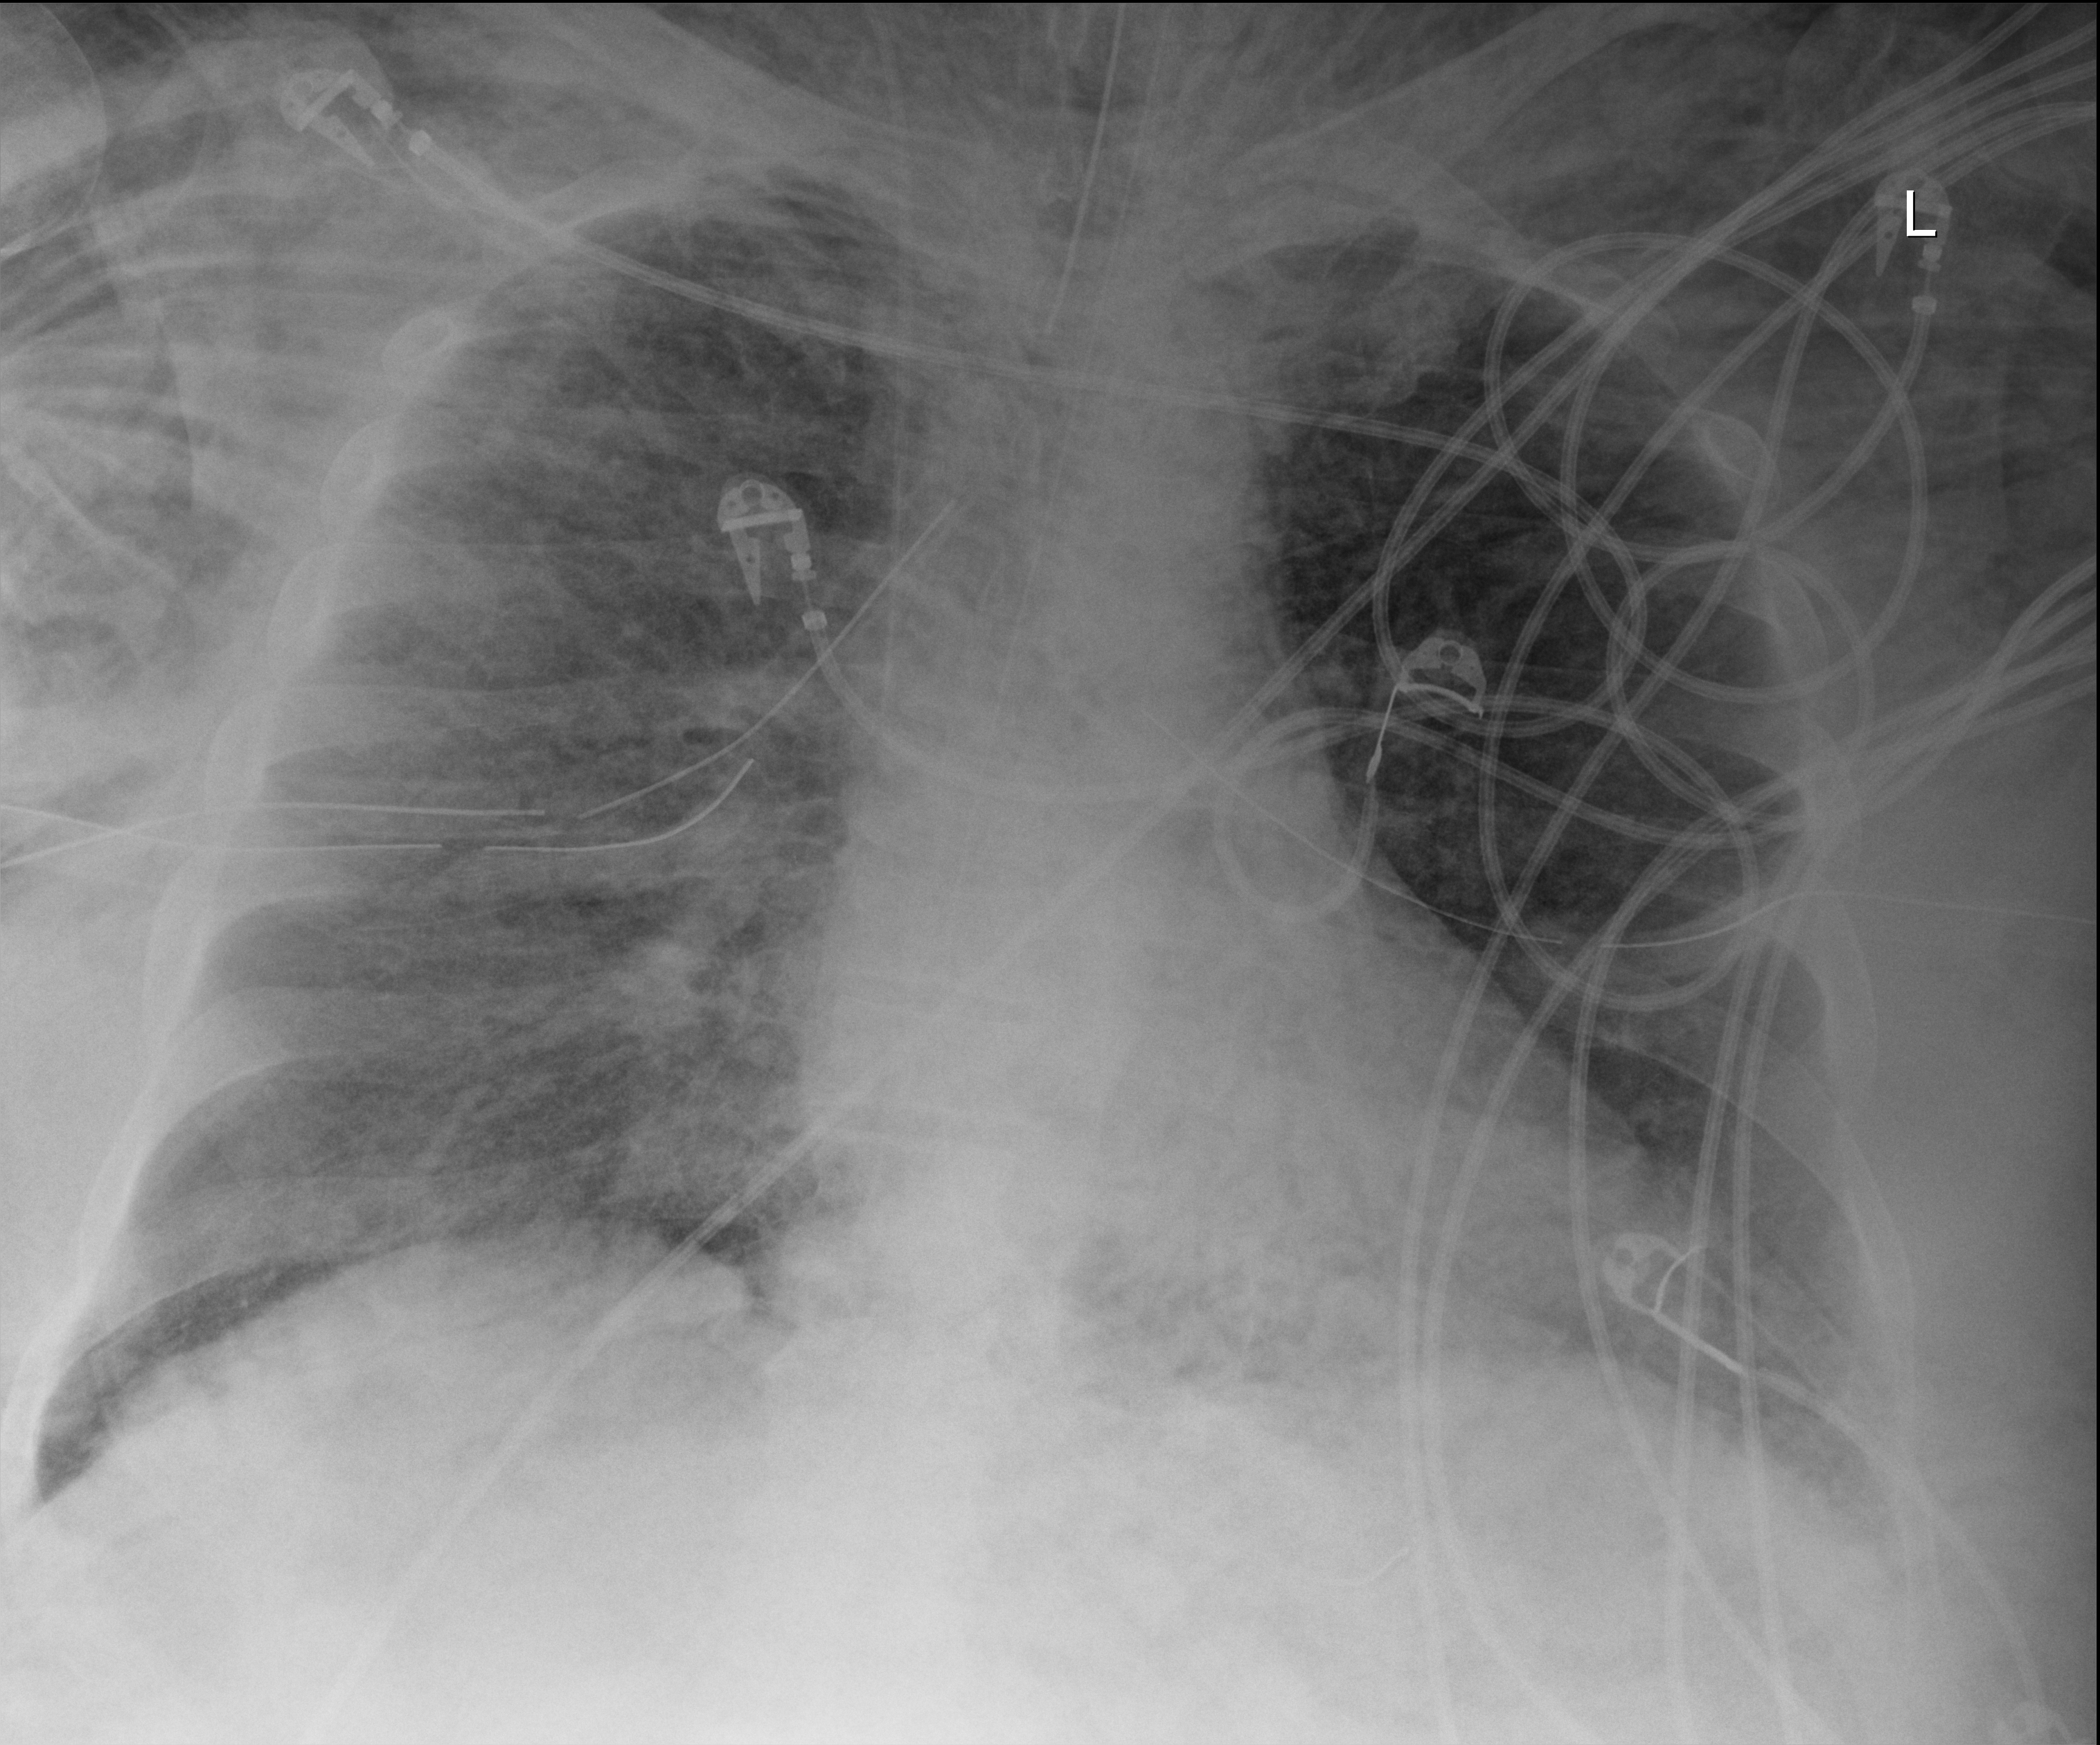
Portable chest radiograph, anteroposterior (AP) projection. Patient hospitalised with COVID-19, aged 18–59 years.
Hospital-stay facts (about this admission, not read from this image; timing relative to this image not recorded): mechanically ventilated during this hospital stay: yes; length of hospital stay: 26 days.